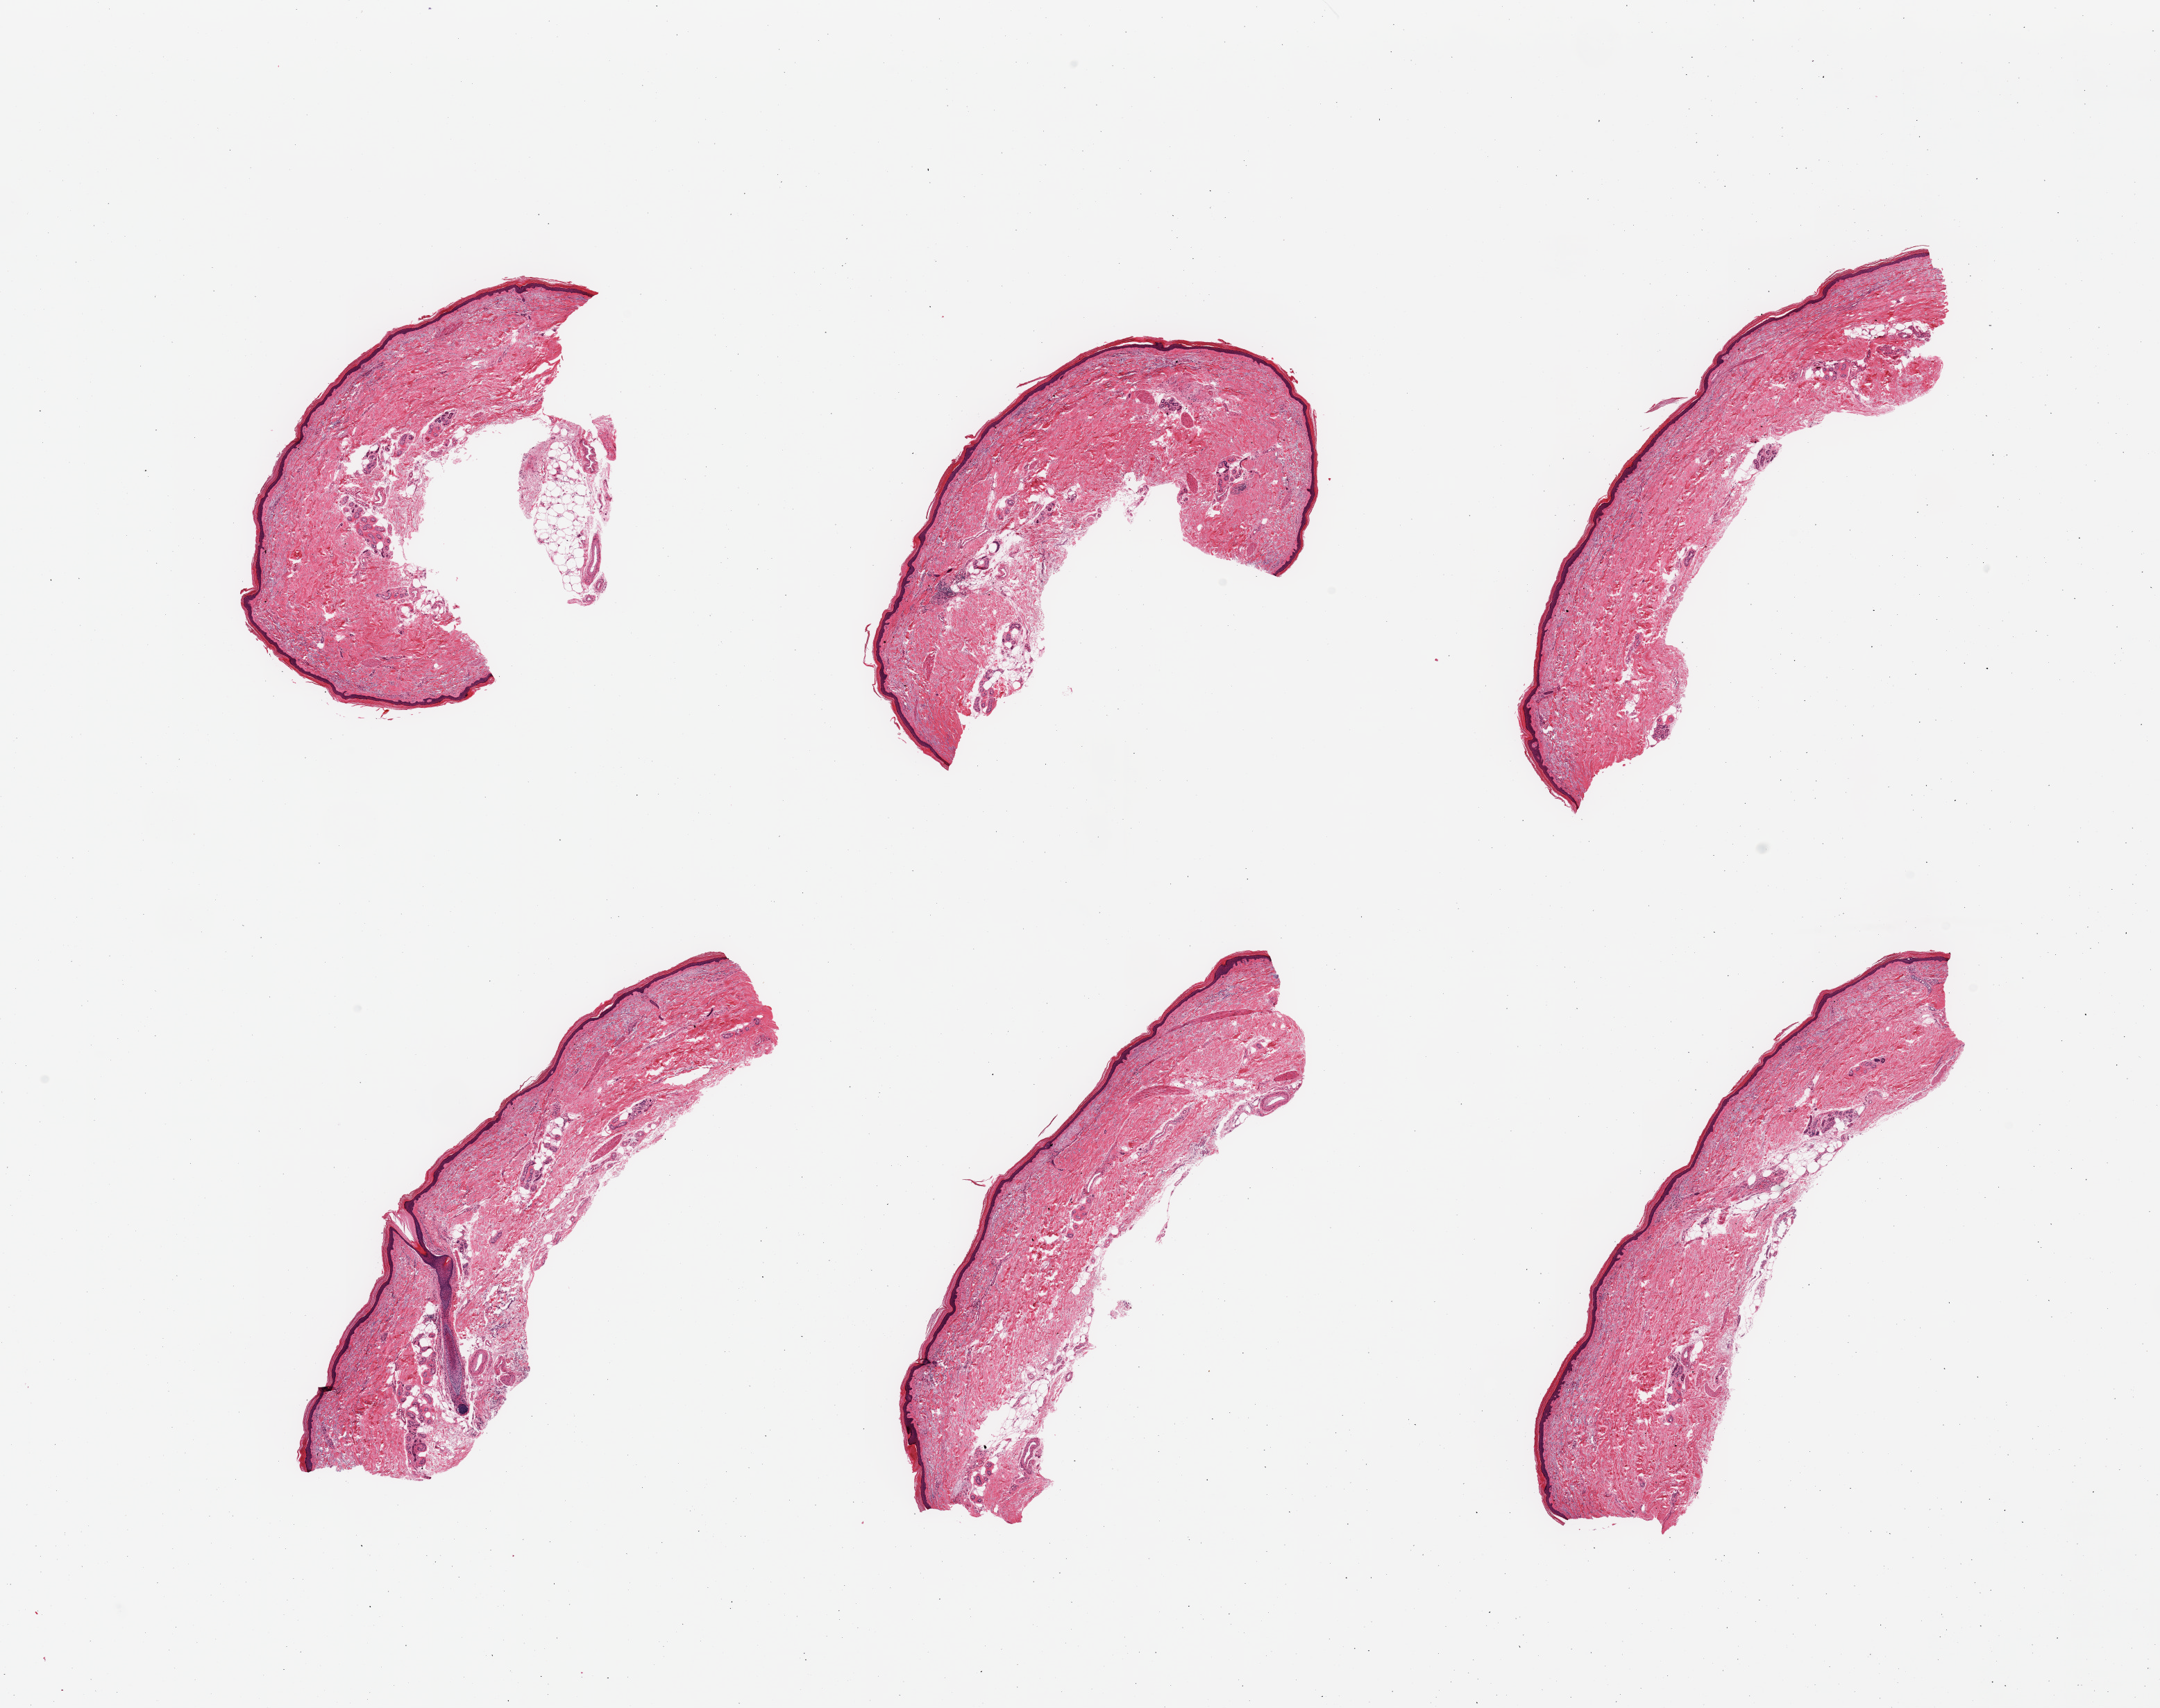
Whole-slide image, haematoxylin and eosin stain — a low-resolution overview of the entire scanned area, about 24.6 x 19.5 mm. PAXgene-fixed paraffin-embedded (PFPE) section. Target tissue: skin of lower leg. Donor tissue sample. Female donor.
Review note (as recorded): 6 pieces; well trimmed; 10% dermal fat.